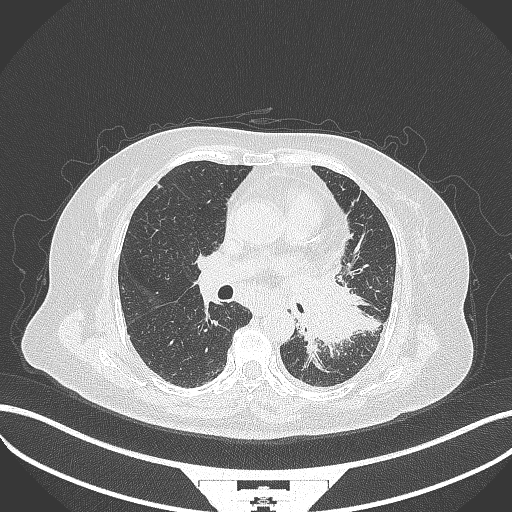
Chest CT, one axial slice; position 186 of 322 along the scan axis; 120 kVp; lung window (W 1500 / L -600 HU); 1 mm slice thickness; 512 × 512 image matrix, field of view 400 × 400 mm. Female patient, age 69 years. From the clinical record (not read from this slice): clinical TNM (as recorded): T2b N3 M1.
Structures marked on this image (bounding box drawn by a radiologist):
- lung tumour (recorded histology: adenocarcinoma): bounding box [x1, y1, x2, y2] px = [300, 275, 362, 351]